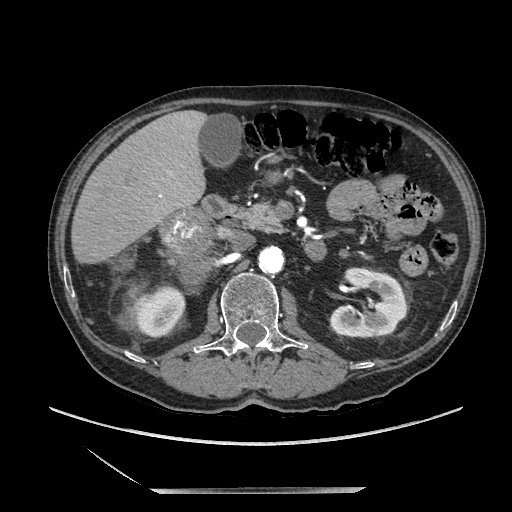
Contrast-enhanced abdominal CT, one axial slice; slice 98 of 243 in the series (ordered by position); soft-tissue window (W 400 / L 40 HU); 512 × 512 image matrix, field of view 420 × 420 mm. Male patient. Case-level facts recorded for this patient, not image findings: diagnosis: adrenocortical carcinoma; tumour side: right adrenal; tumour size at pathology: 16 cm; Ki-67 index: 17 %; stage (as recorded): 3.
Structures marked on this image (semi-automatically segmented with operator editing):
- mass: bounding box [x1, y1, x2, y2] px = [164, 211, 213, 280]